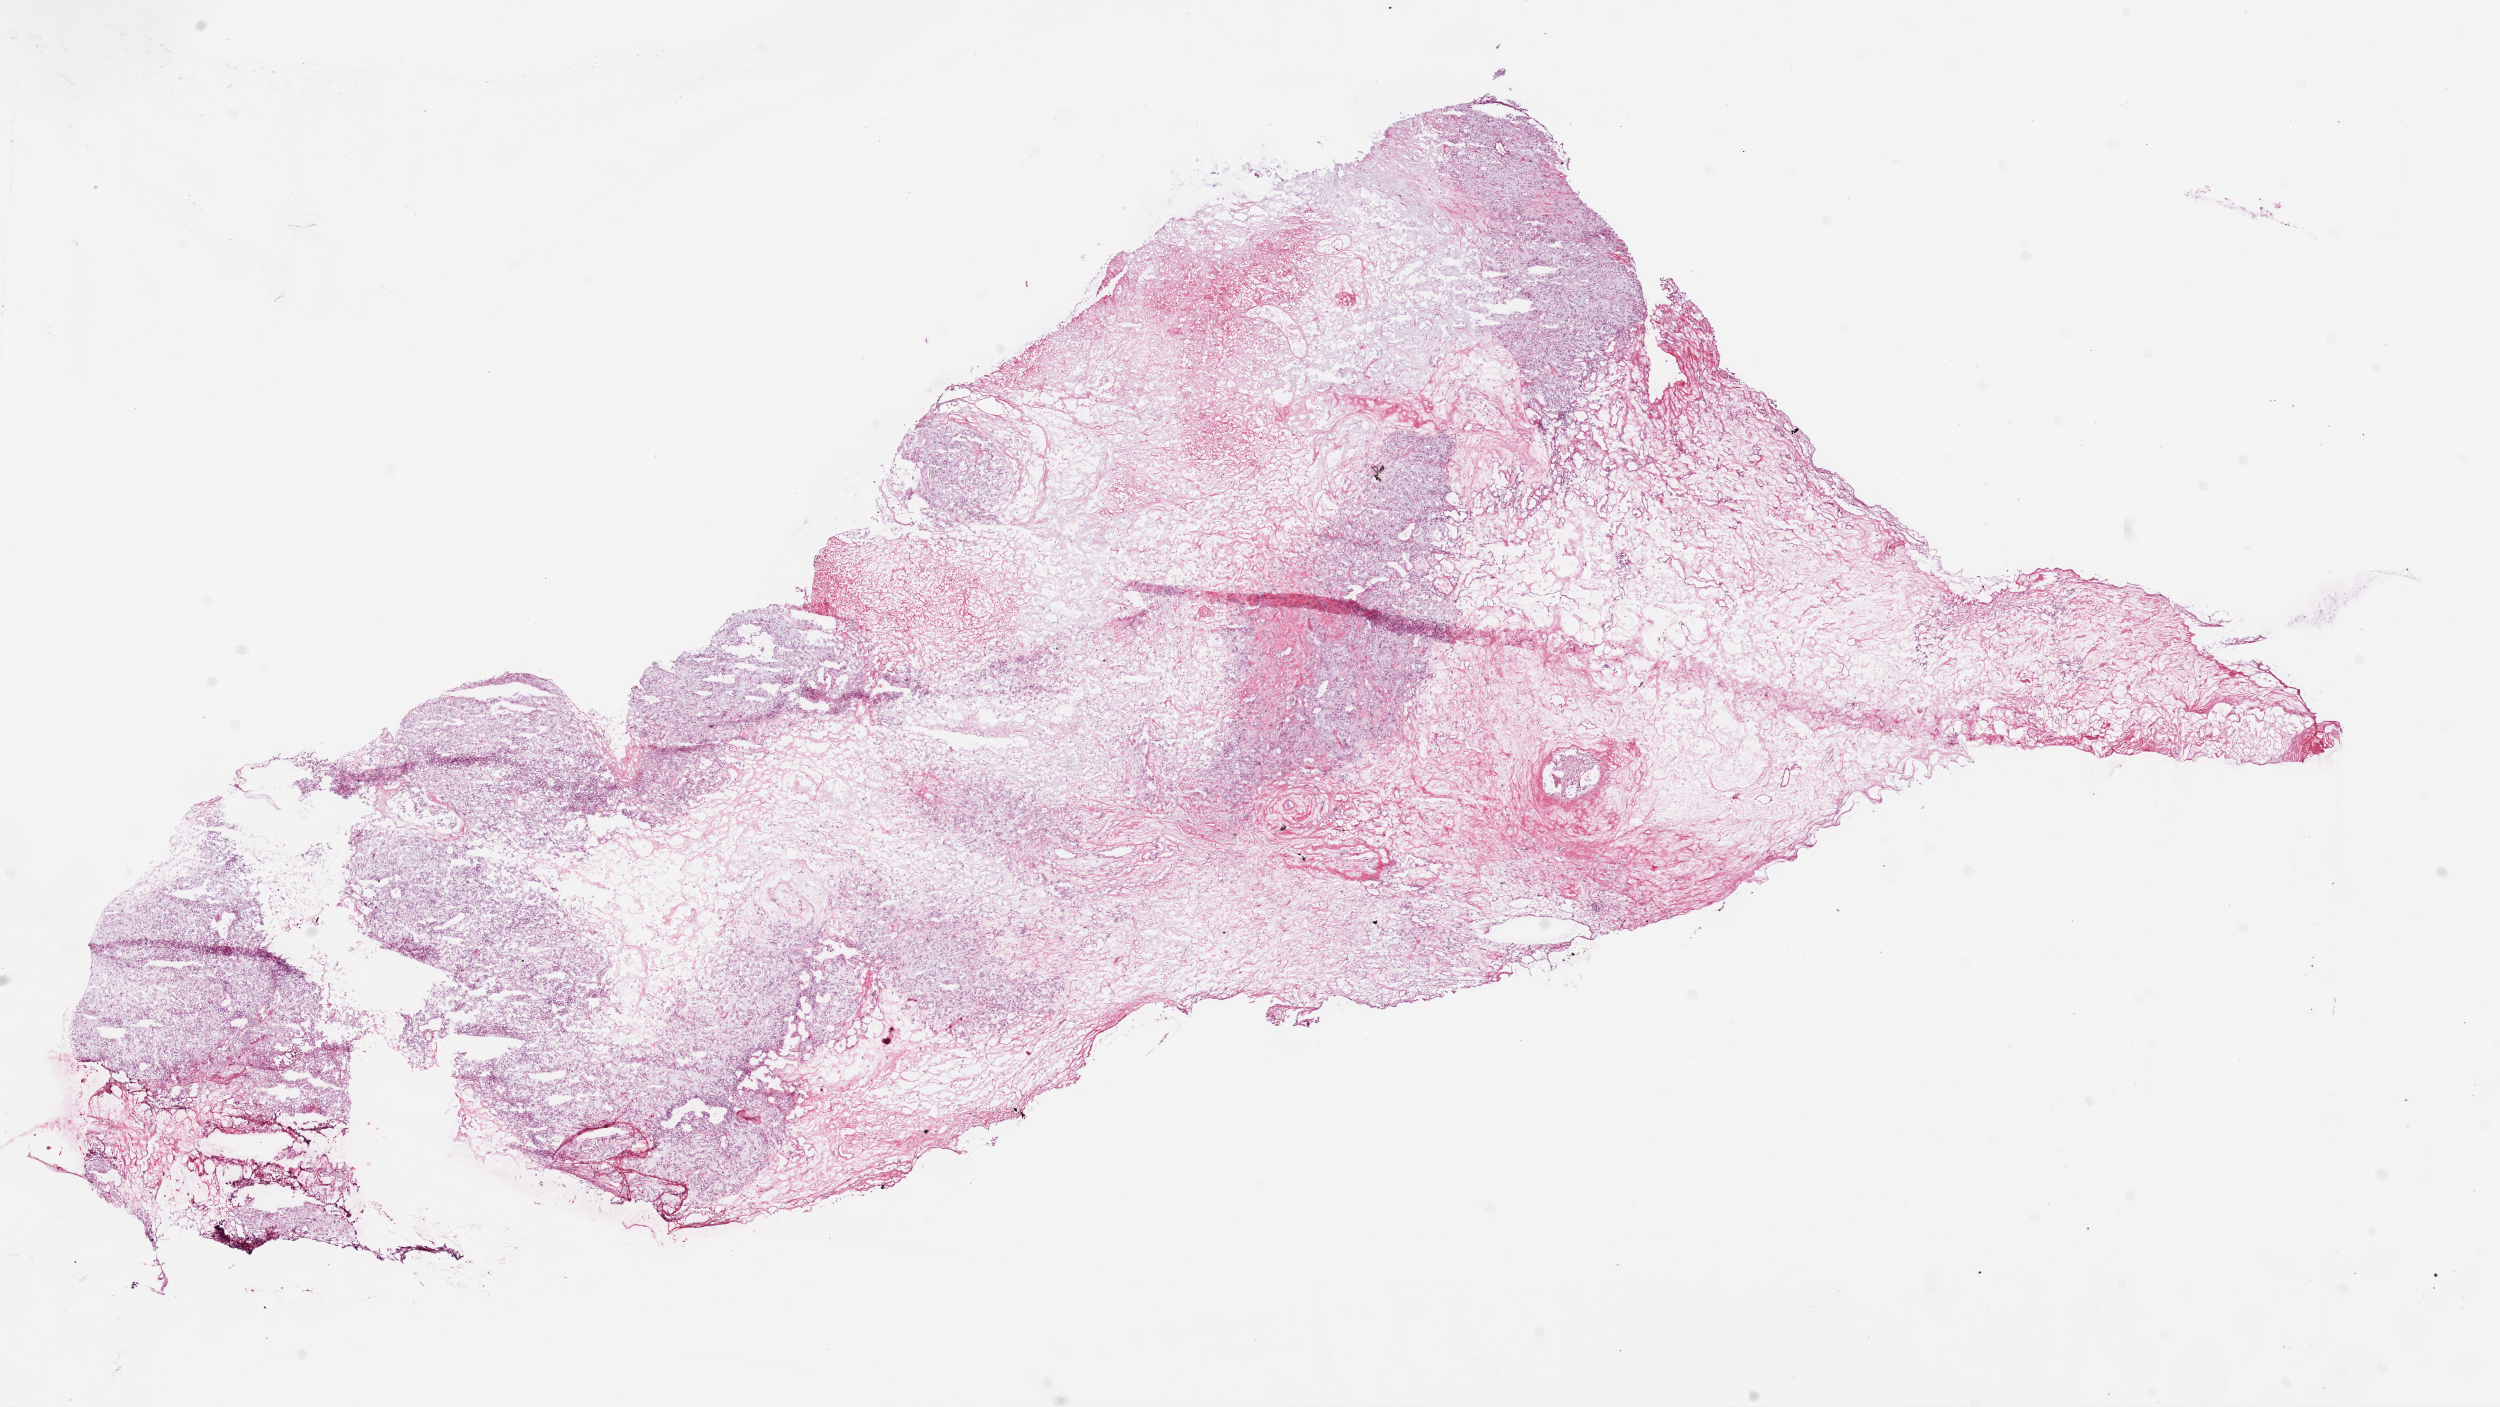
Whole-slide histology image, Hematoxylin and eosin (H&E) stained, a low-resolution overview of the entire scanned area, about 20.1 x 11.3 mm; frozen section; primary tumour sample from the kidney. Female patient; age at initial diagnosis 72 years. Histologic grade: GX (grade cannot be assessed). Pathologist review of this section (percent, as recorded): tumour cells 22%, tumour nuclei 70%, normal cells 0%, stromal cells 70%, necrosis 8%.
- AJCC pathologic stage: III (5th edition)
- lymph nodes positive (case pathology): 1 of 1 examined
- pathologic diagnosis: Clear cell adenocarcinoma, NOS
- TNM: T3a N1 M0